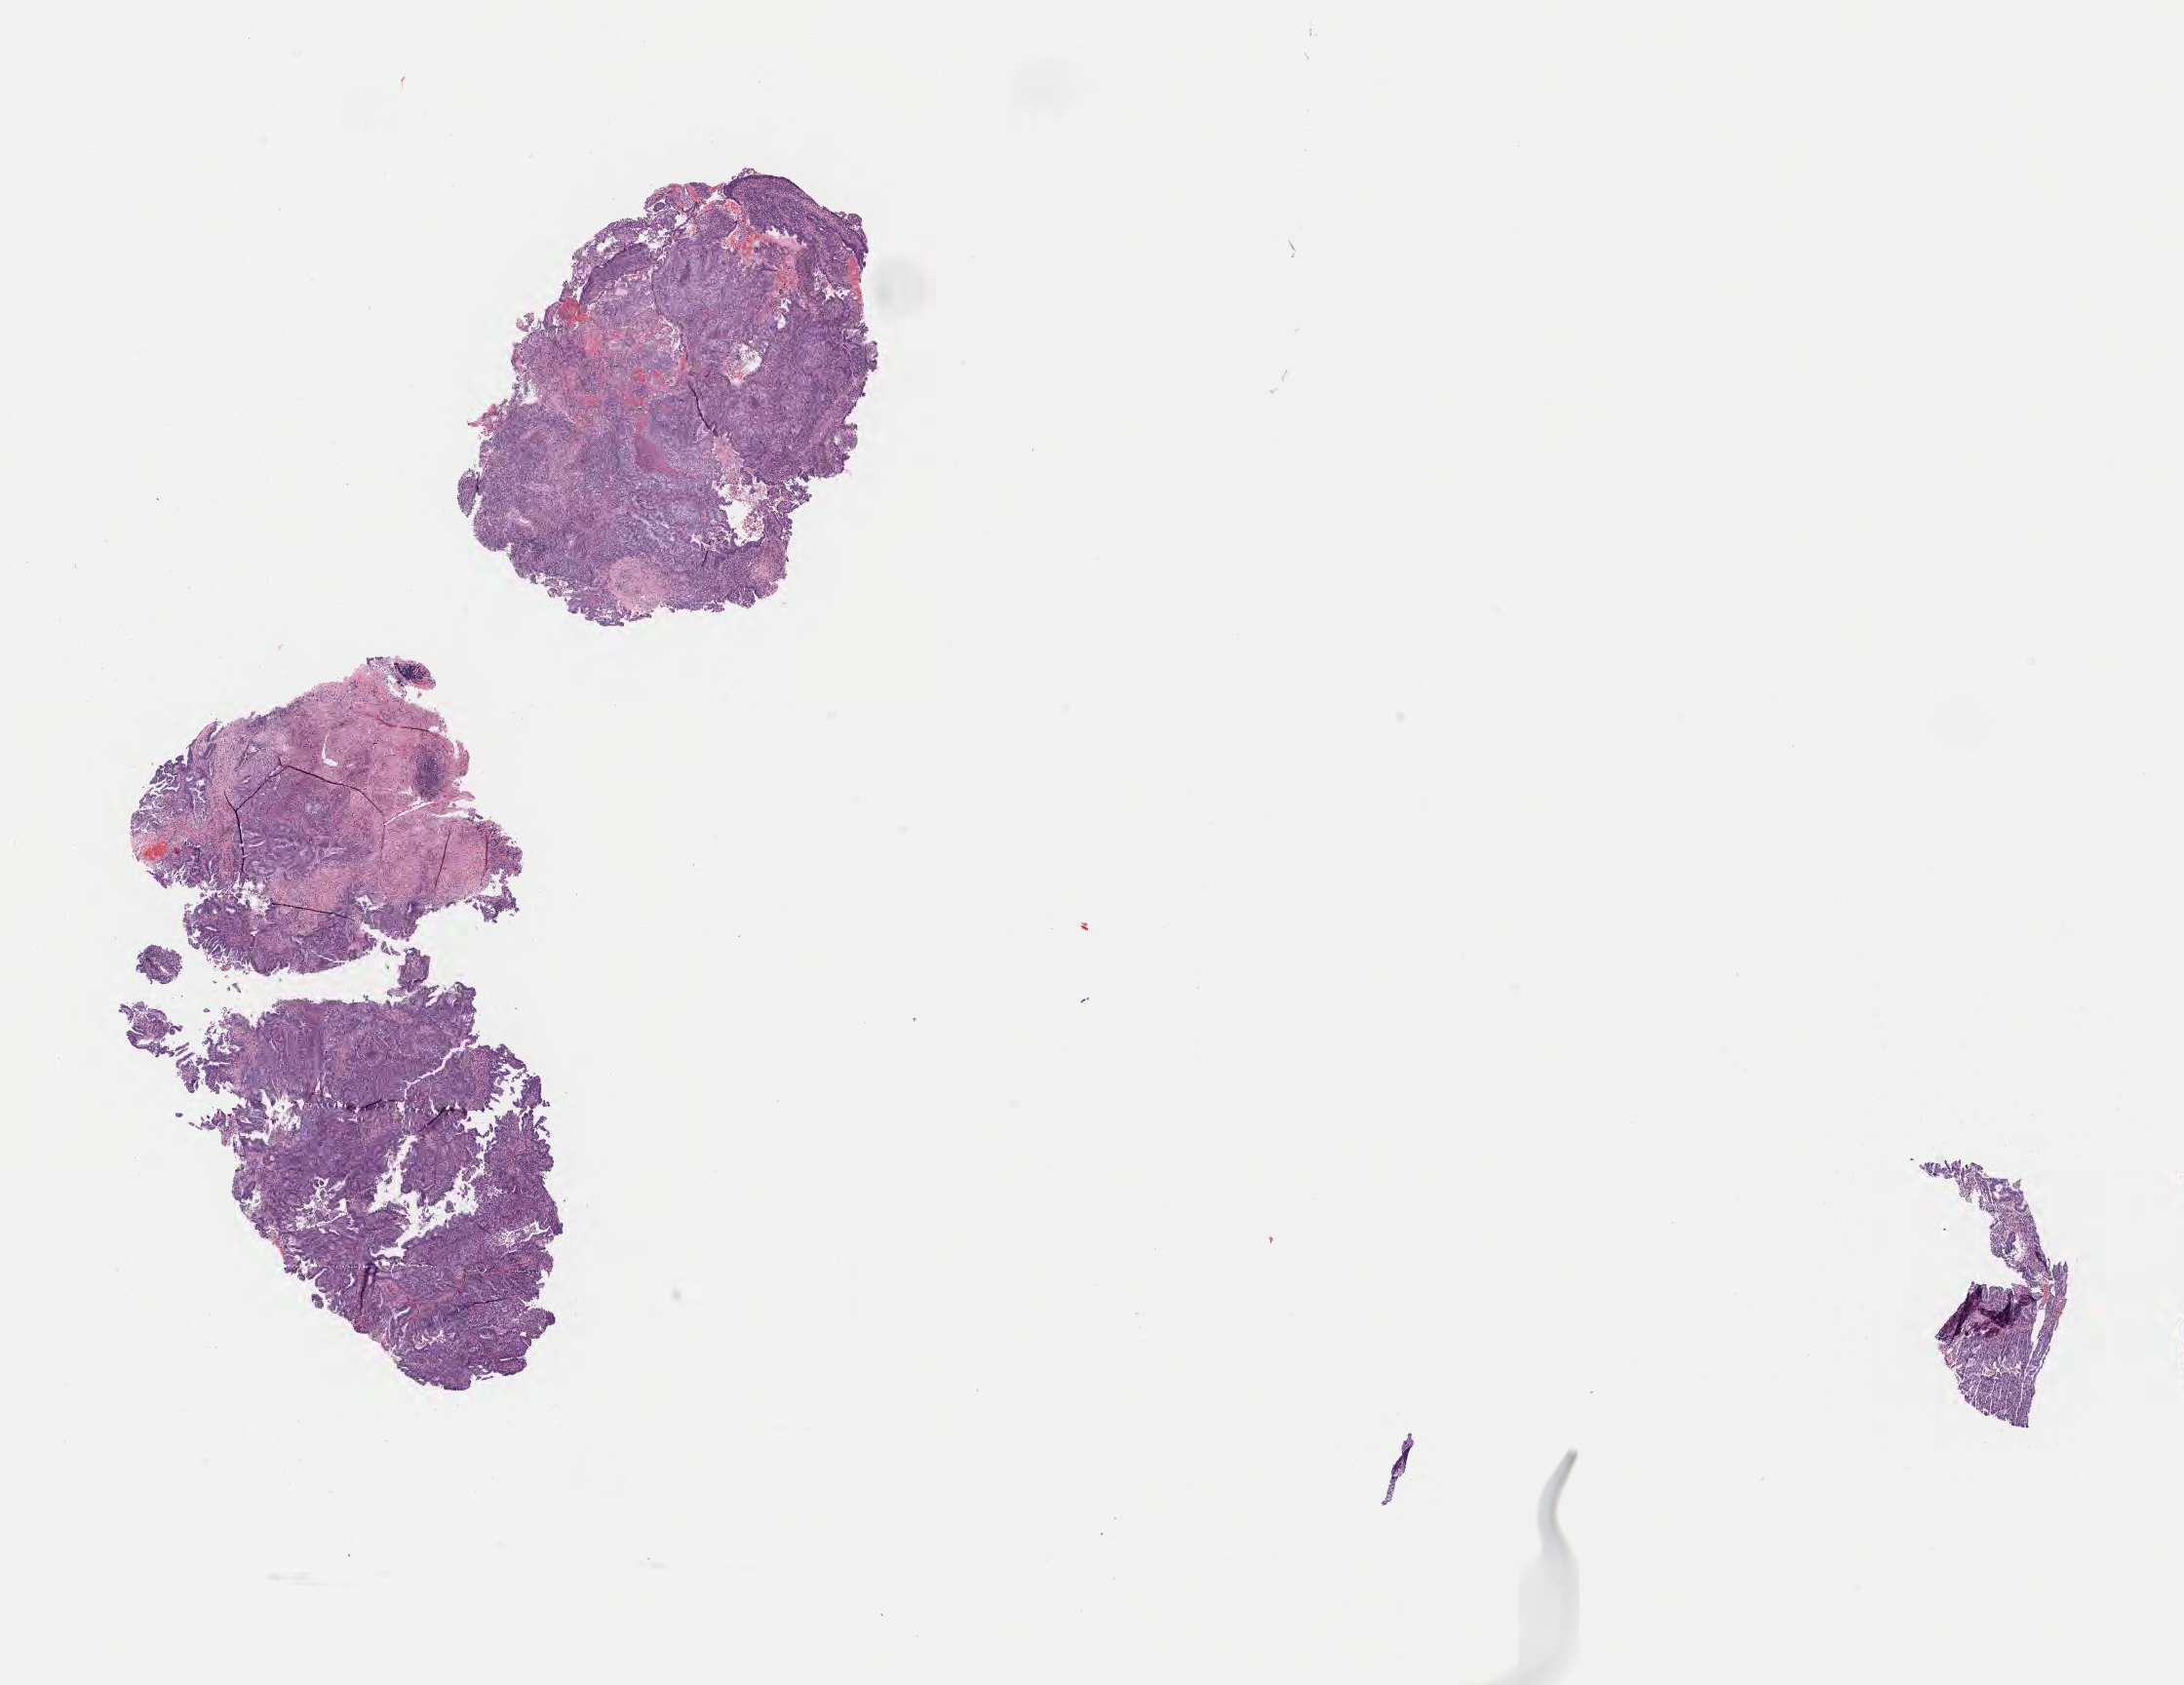
Whole-slide image, H&E stain, a low-resolution overview of the entire scanned area, about 18.1 x 14.0 mm, specimen: tumor tissue, anatomic site: cervix. Female patient, aged 48.
Histologic diagnosis: Adenocarcinoma, NOS.